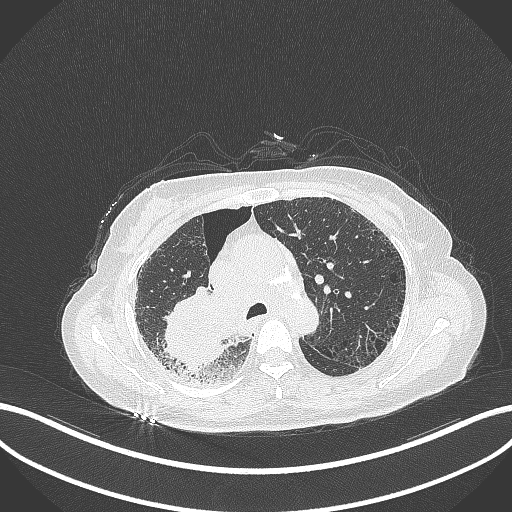
Chest CT, one axial slice. Slice 235 of 408 in the series (ordered by position). Reconstruction kernel B70f. 120 kVp. Lung window (W 1500 / L -600 HU). 1 mm slice thickness. 512 × 512 image matrix, field of view 400 × 400 mm. Female patient, age 64 years. Case-level facts recorded for this patient, not image findings: clinical TNM (as recorded): T3 N3 M0.
Outlined on this slice (bounding box drawn by a radiologist):
- lung tumour (recorded histology: squamous cell carcinoma): bounding box (x1, y1, x2, y2) in pixels: (162, 283, 231, 377)